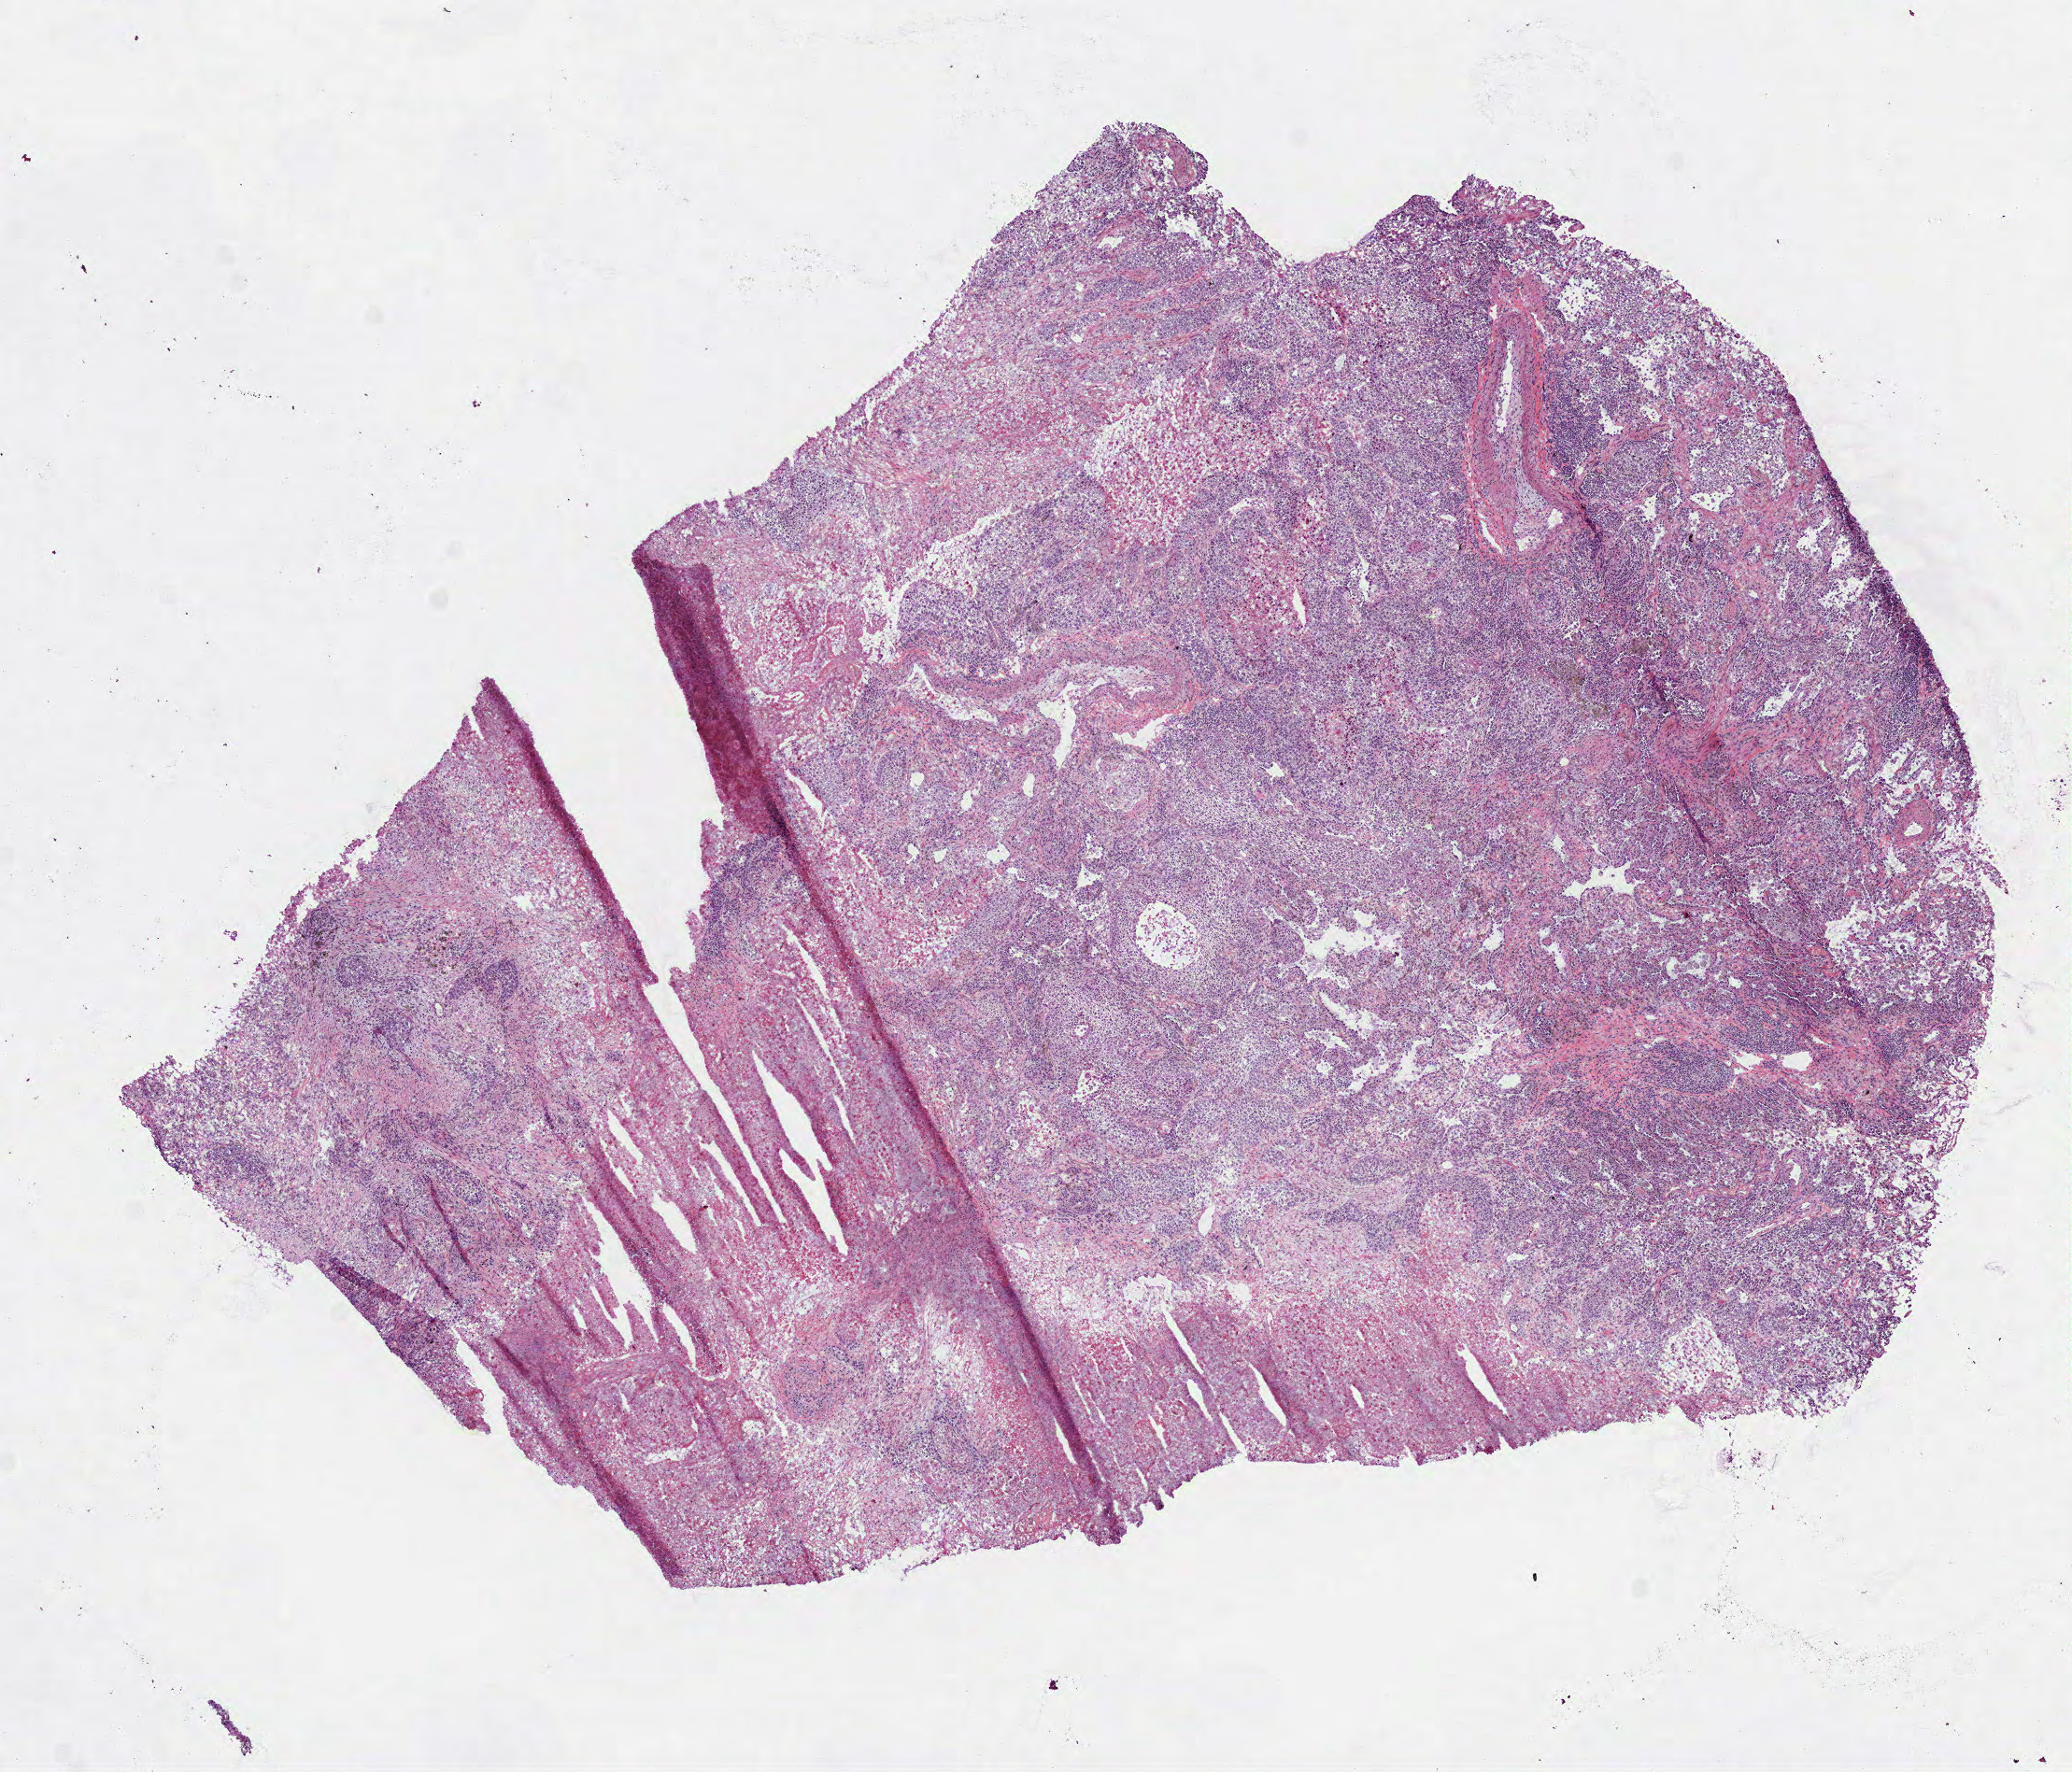
H&E whole-slide image, a low-resolution overview of the entire scanned area, about 8.9 x 7.6 mm (slide scanned at 40x). Frozen section from the bottom of the tissue portion. Lung, primary tumour sample. Female patient. Slide review estimates, as recorded: tumour cells 53%, tumour nuclei 50%, normal cells 17%, stromal cells 0%, necrosis 30%. Infiltration values recorded for this section: lymphocyte infiltration 30%, monocyte infiltration 0%, neutrophil infiltration 5%.
- AJCC pathologic stage: IA (6th edition)
- pathologic diagnosis: Squamous cell carcinoma, NOS (upper lobe, lung)